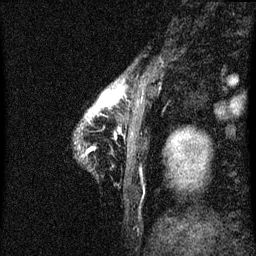
Breast MRI (dynamic contrast-enhanced), one sagittal slice; position 5 of 60 along the scan axis; dynamic contrast-enhanced series, image 2 of 3 at this slice position (ordered by acquisition); 1.5 T; TE 4.2 ms, TR 8 ms; 2 mm slice thickness; 256 × 256 image matrix. Female patient, age 38 years.
Annotated regions visible in this slice (semi-automatically segmented with operator editing):
- analysis volume of interest (the breast-tissue region the enhancement analysis was run in; not a lesion): box from (x=92, y=88) to (x=119, y=131) px
- tumour enhancement mask (voxels above the 70 % enhancement threshold inside the analysis volume of interest): (x=96, y=92)–(x=118, y=111)